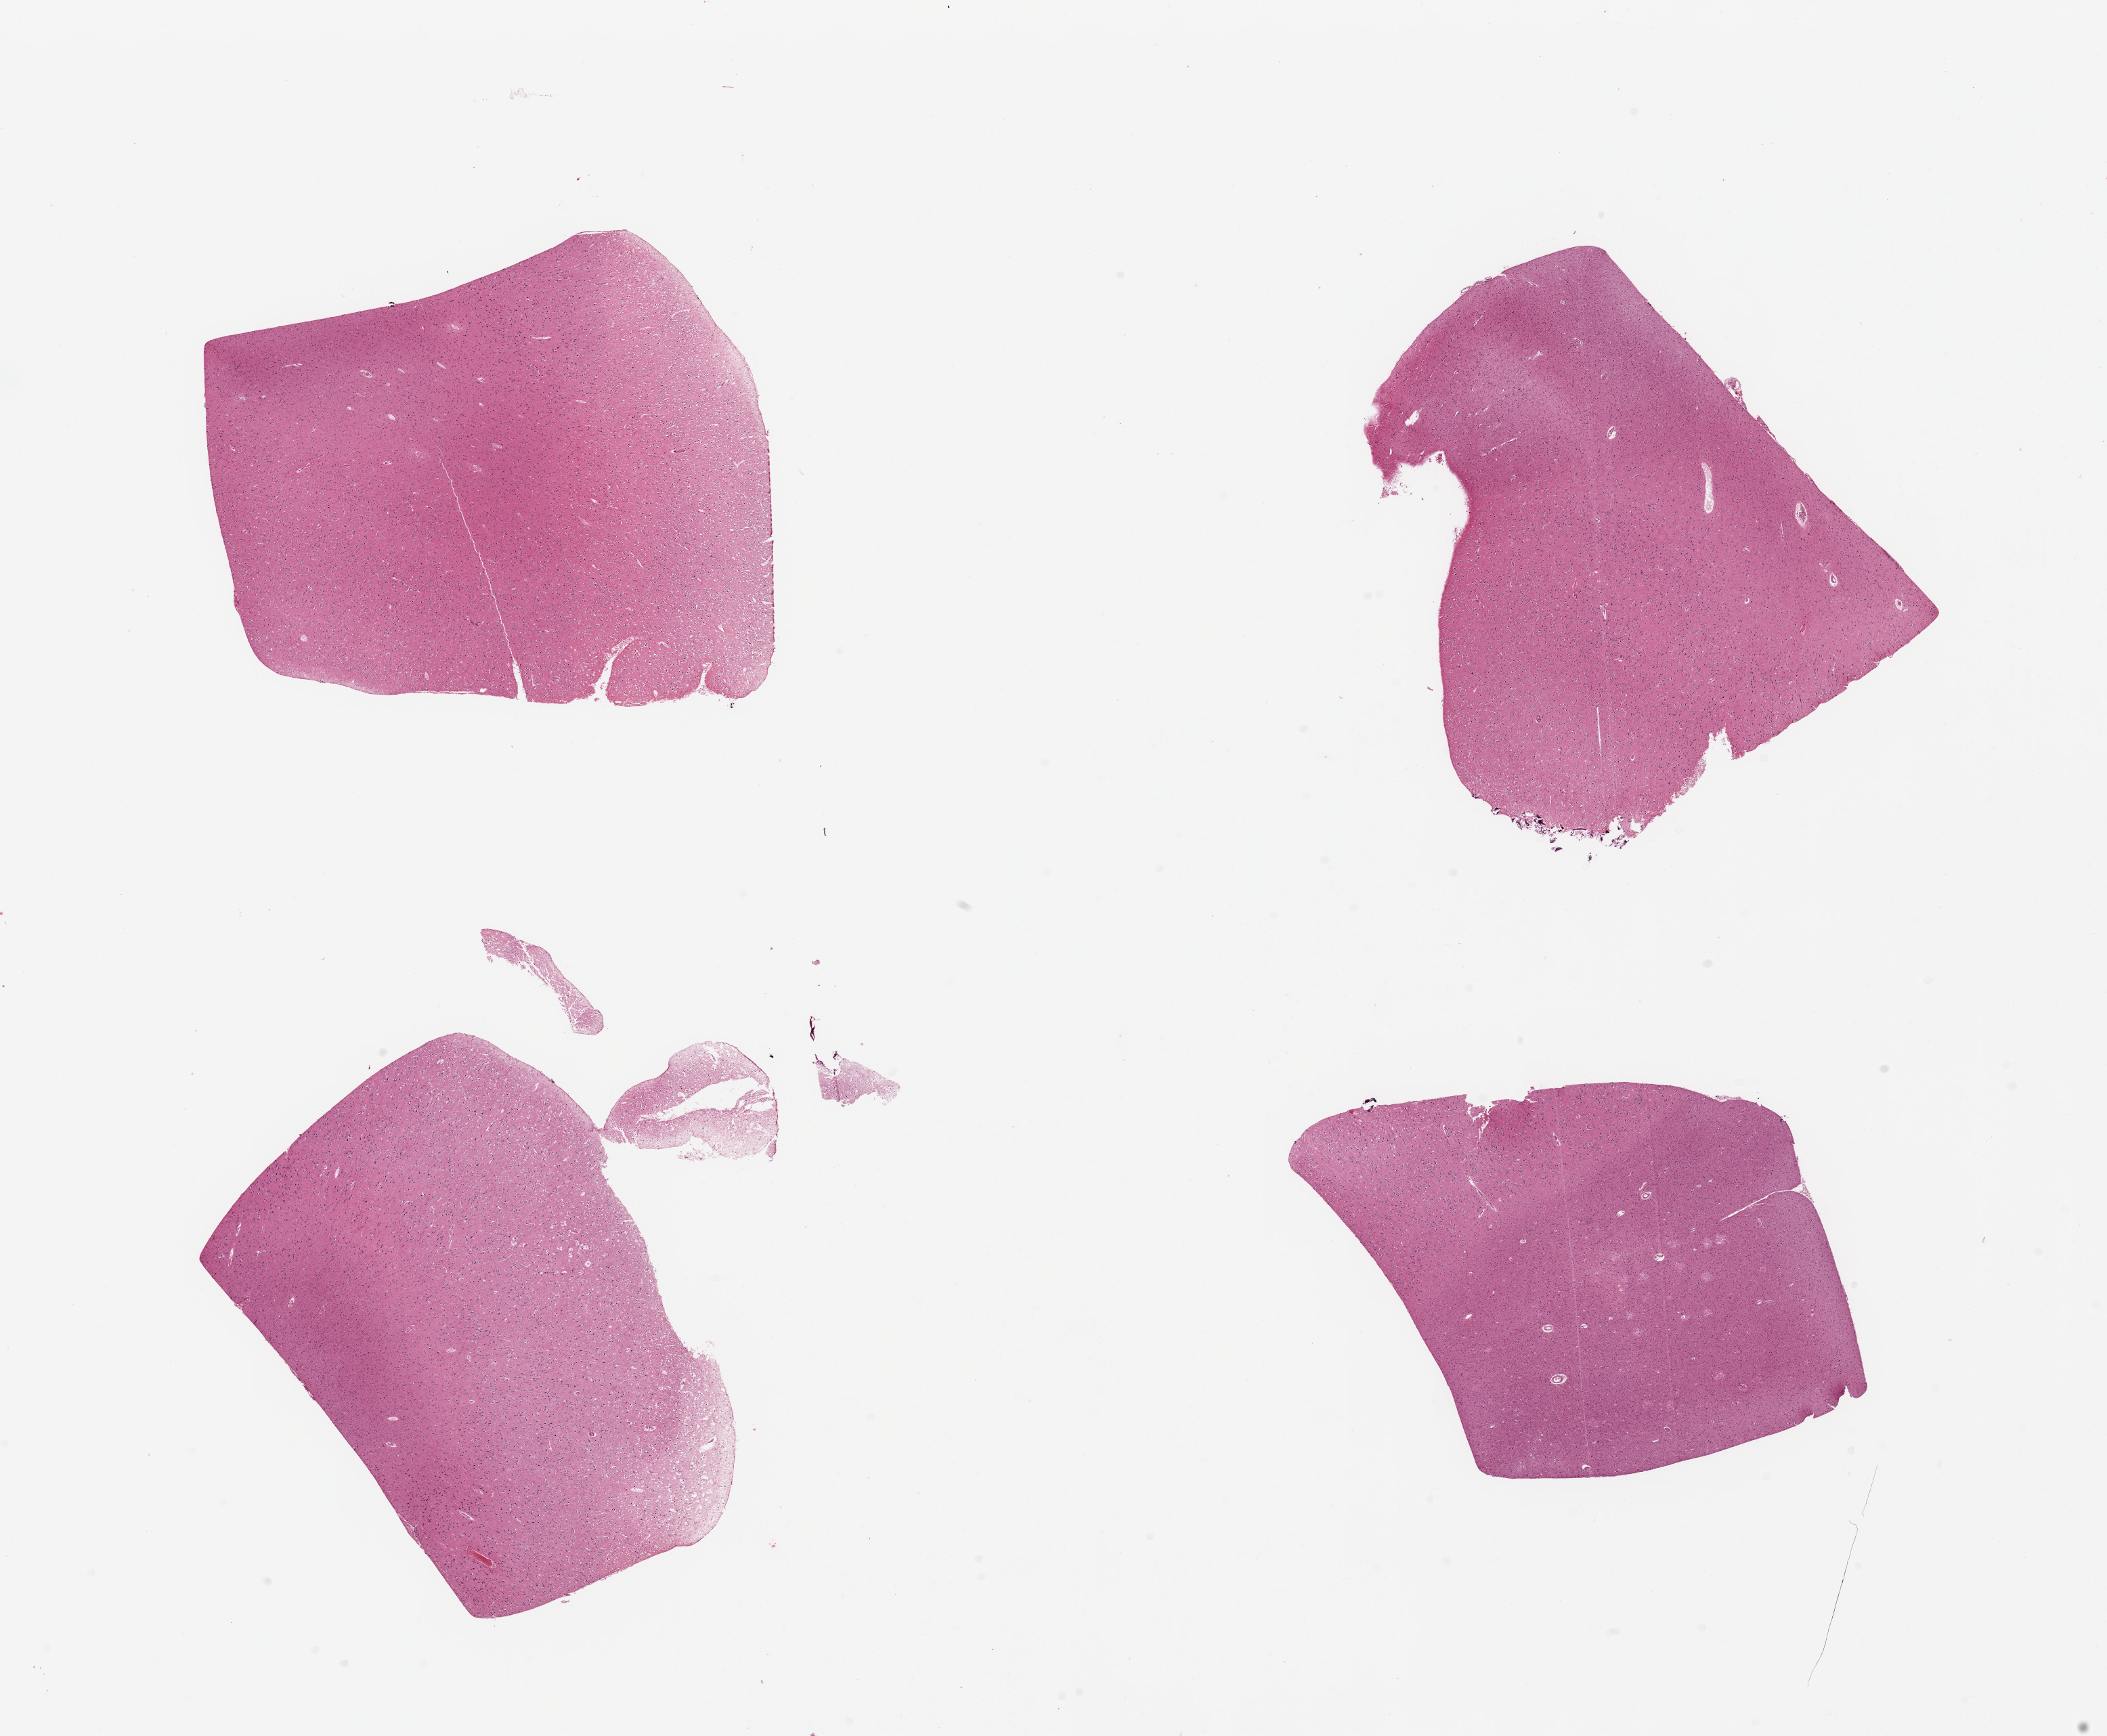
Whole-slide image, H&E stain — a low-resolution overview of the entire scanned area, about 24.6 x 20.3 mm, PAXgene-fixed, paraffin-embedded tissue, section of cerebral cortex (target tissue), donor tissue sample.
* reviewer comment on this tissue sample: 4 pieces; focal calcifications